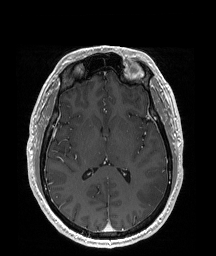
Brain MRI from a brain-tumour surgery series, one axial slice; T1-weighted post-contrast; 1 mm slice thickness; 216 × 256 image matrix, field of view 219 × 260 mm. Case-level facts recorded for this patient, not image findings: histopathology: Glioblastoma; WHO grade: 4; IDH mutation: no; tumour location: Left Temporal Parietal.
Structures marked on this image (outlined manually by an expert reader):
- tumour: bounding box (x1, y1, x2, y2) in pixels: (137, 171, 168, 210)